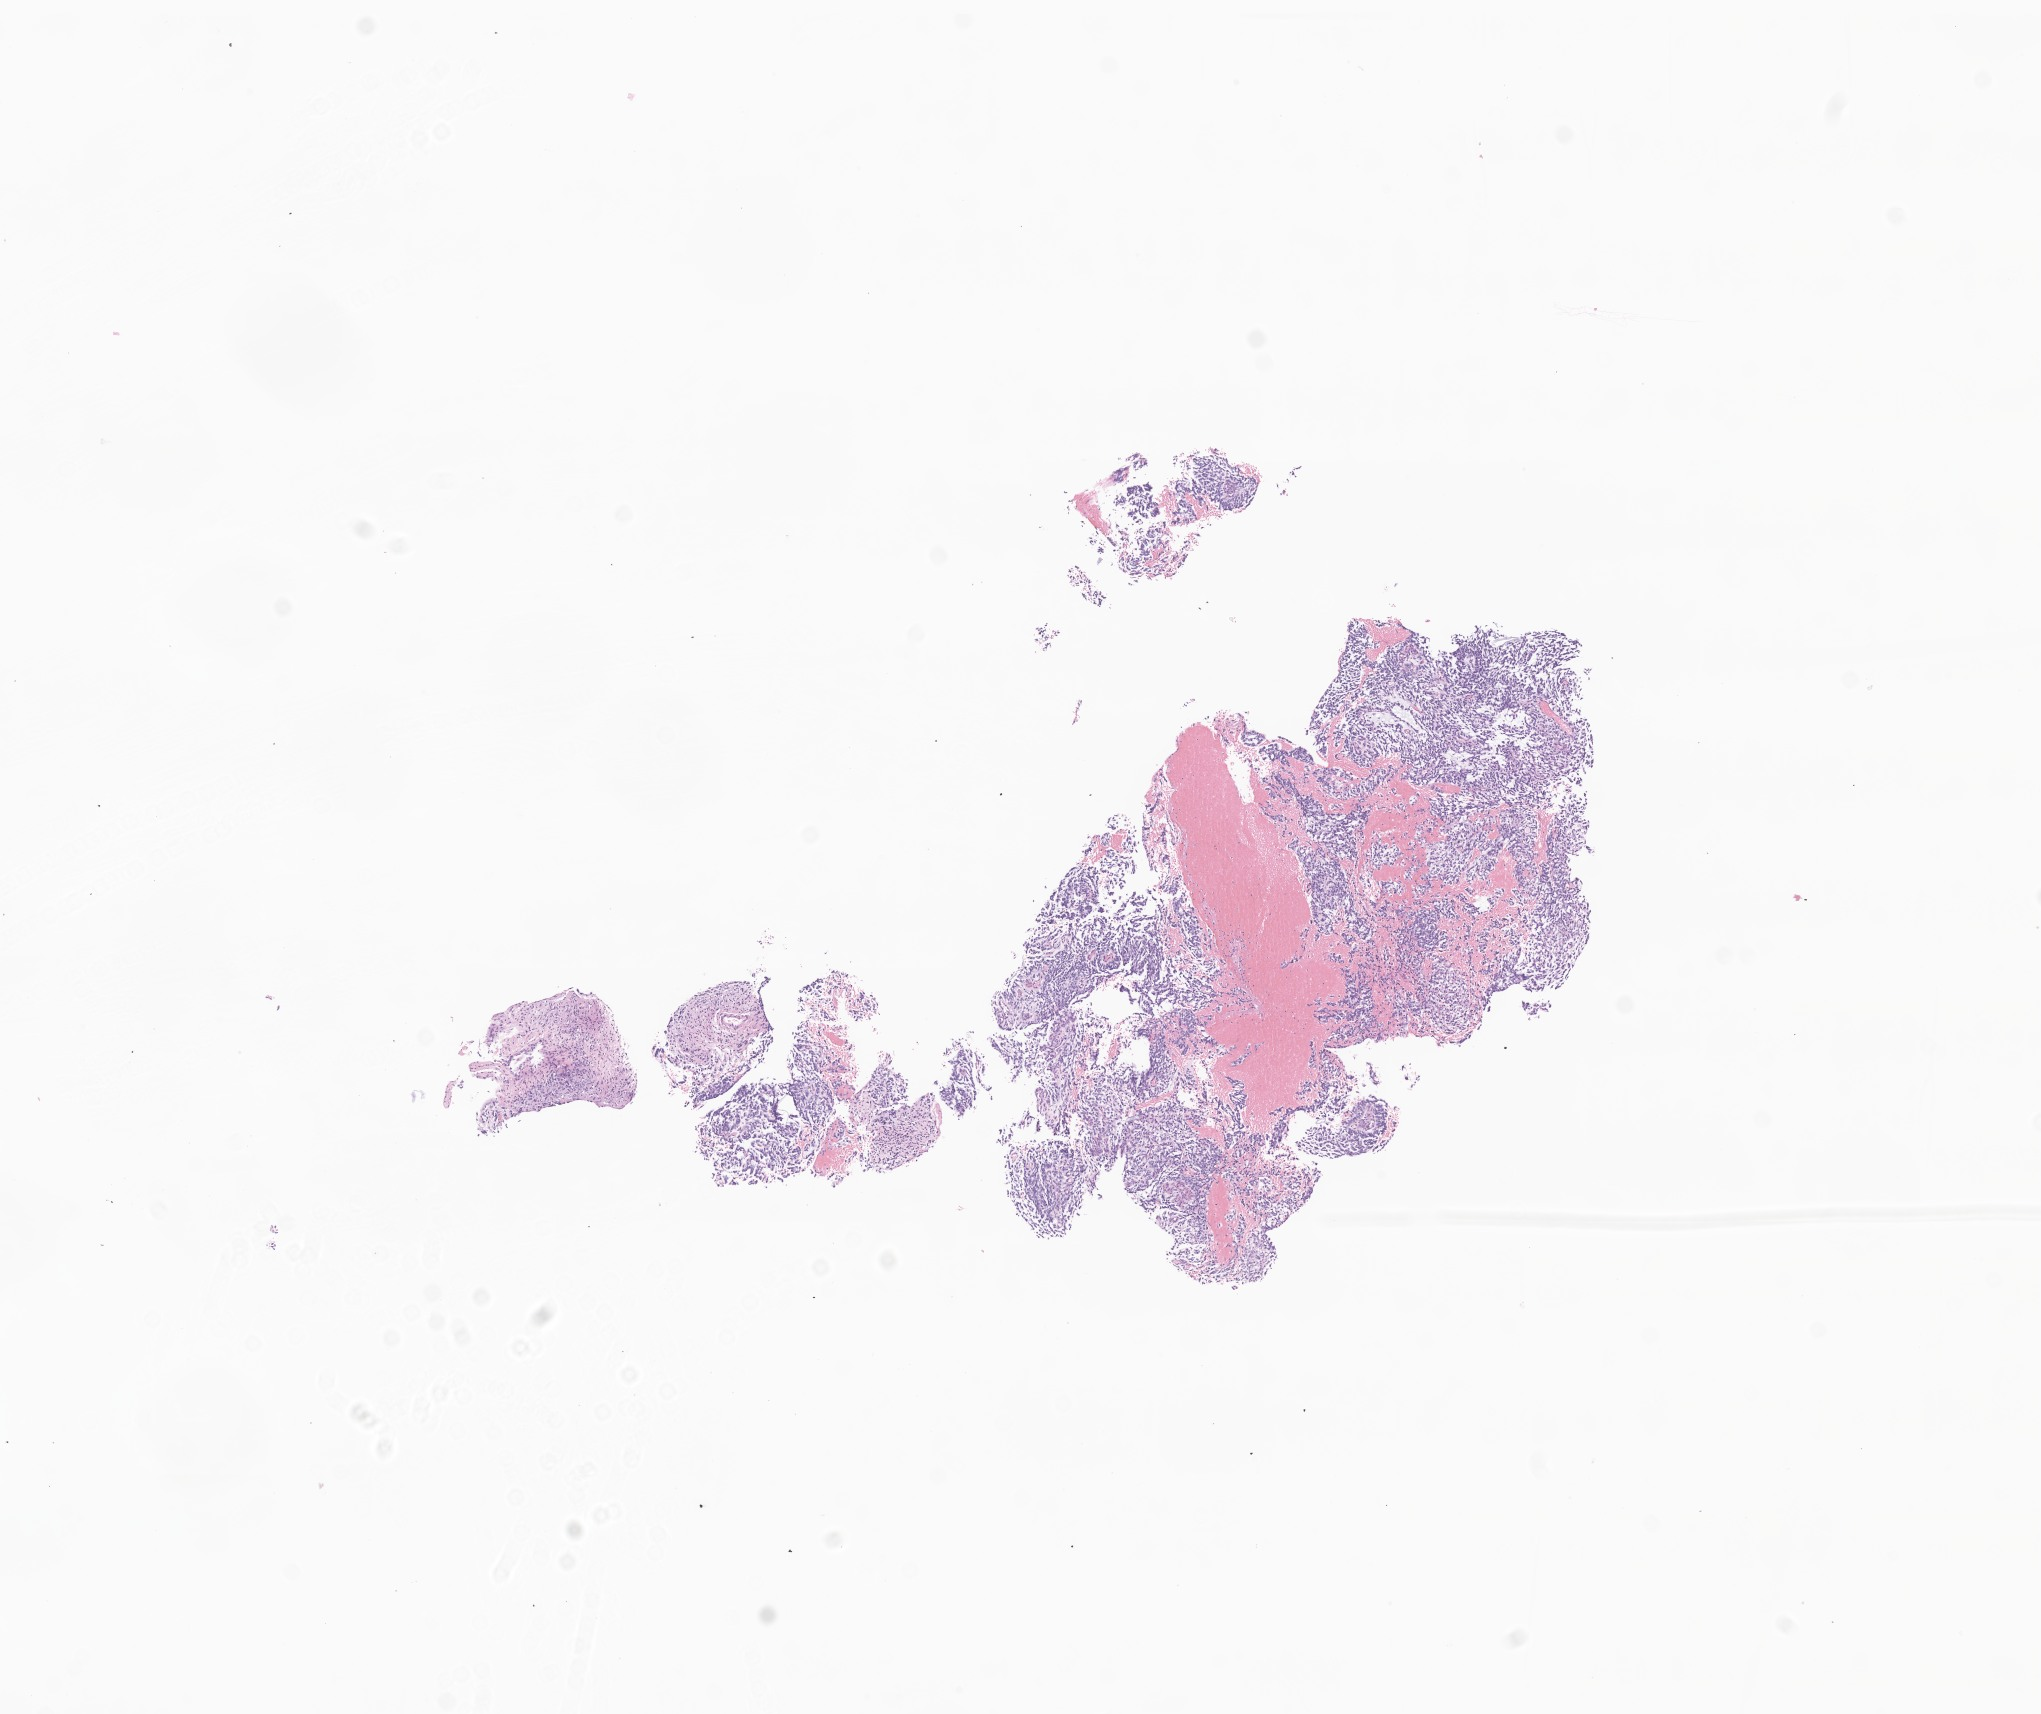
Whole-slide image, H&E stain of tumor tissue from the spinal cord, low-resolution overview of the scanned area, about 8.6 x 7.2 mm, FFPE section. Patient female; age 157 months (13 years 1 month).
• recorded diagnosis: Glioma, malignant